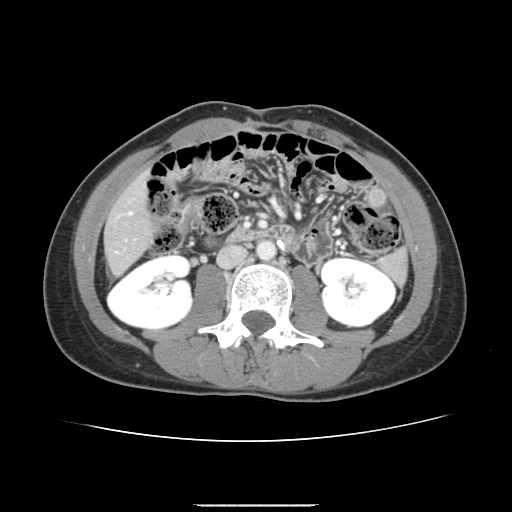
Contrast-enhanced abdominal CT, one axial slice. Slice 46 of 150 in the series (ordered by position). 120 kVp. Intravenous contrast given. Soft-tissue window (W 400 / L 40 HU). 512 × 512 image matrix, field of view 324 × 324 mm. Female patient, age 32 years. From the clinical record (not read from this slice): diagnosis: colorectal cancer liver metastases, imaged before liver resection.
Annotated regions visible in this slice (outlined manually by an expert reader):
- hepatic veins: bounding box [x1, y1, x2, y2] px = [129, 212, 131, 214]
- liver: [106, 178, 152, 273]
- planned liver remnant (the part of the liver to remain after resection): [106, 179, 152, 273]